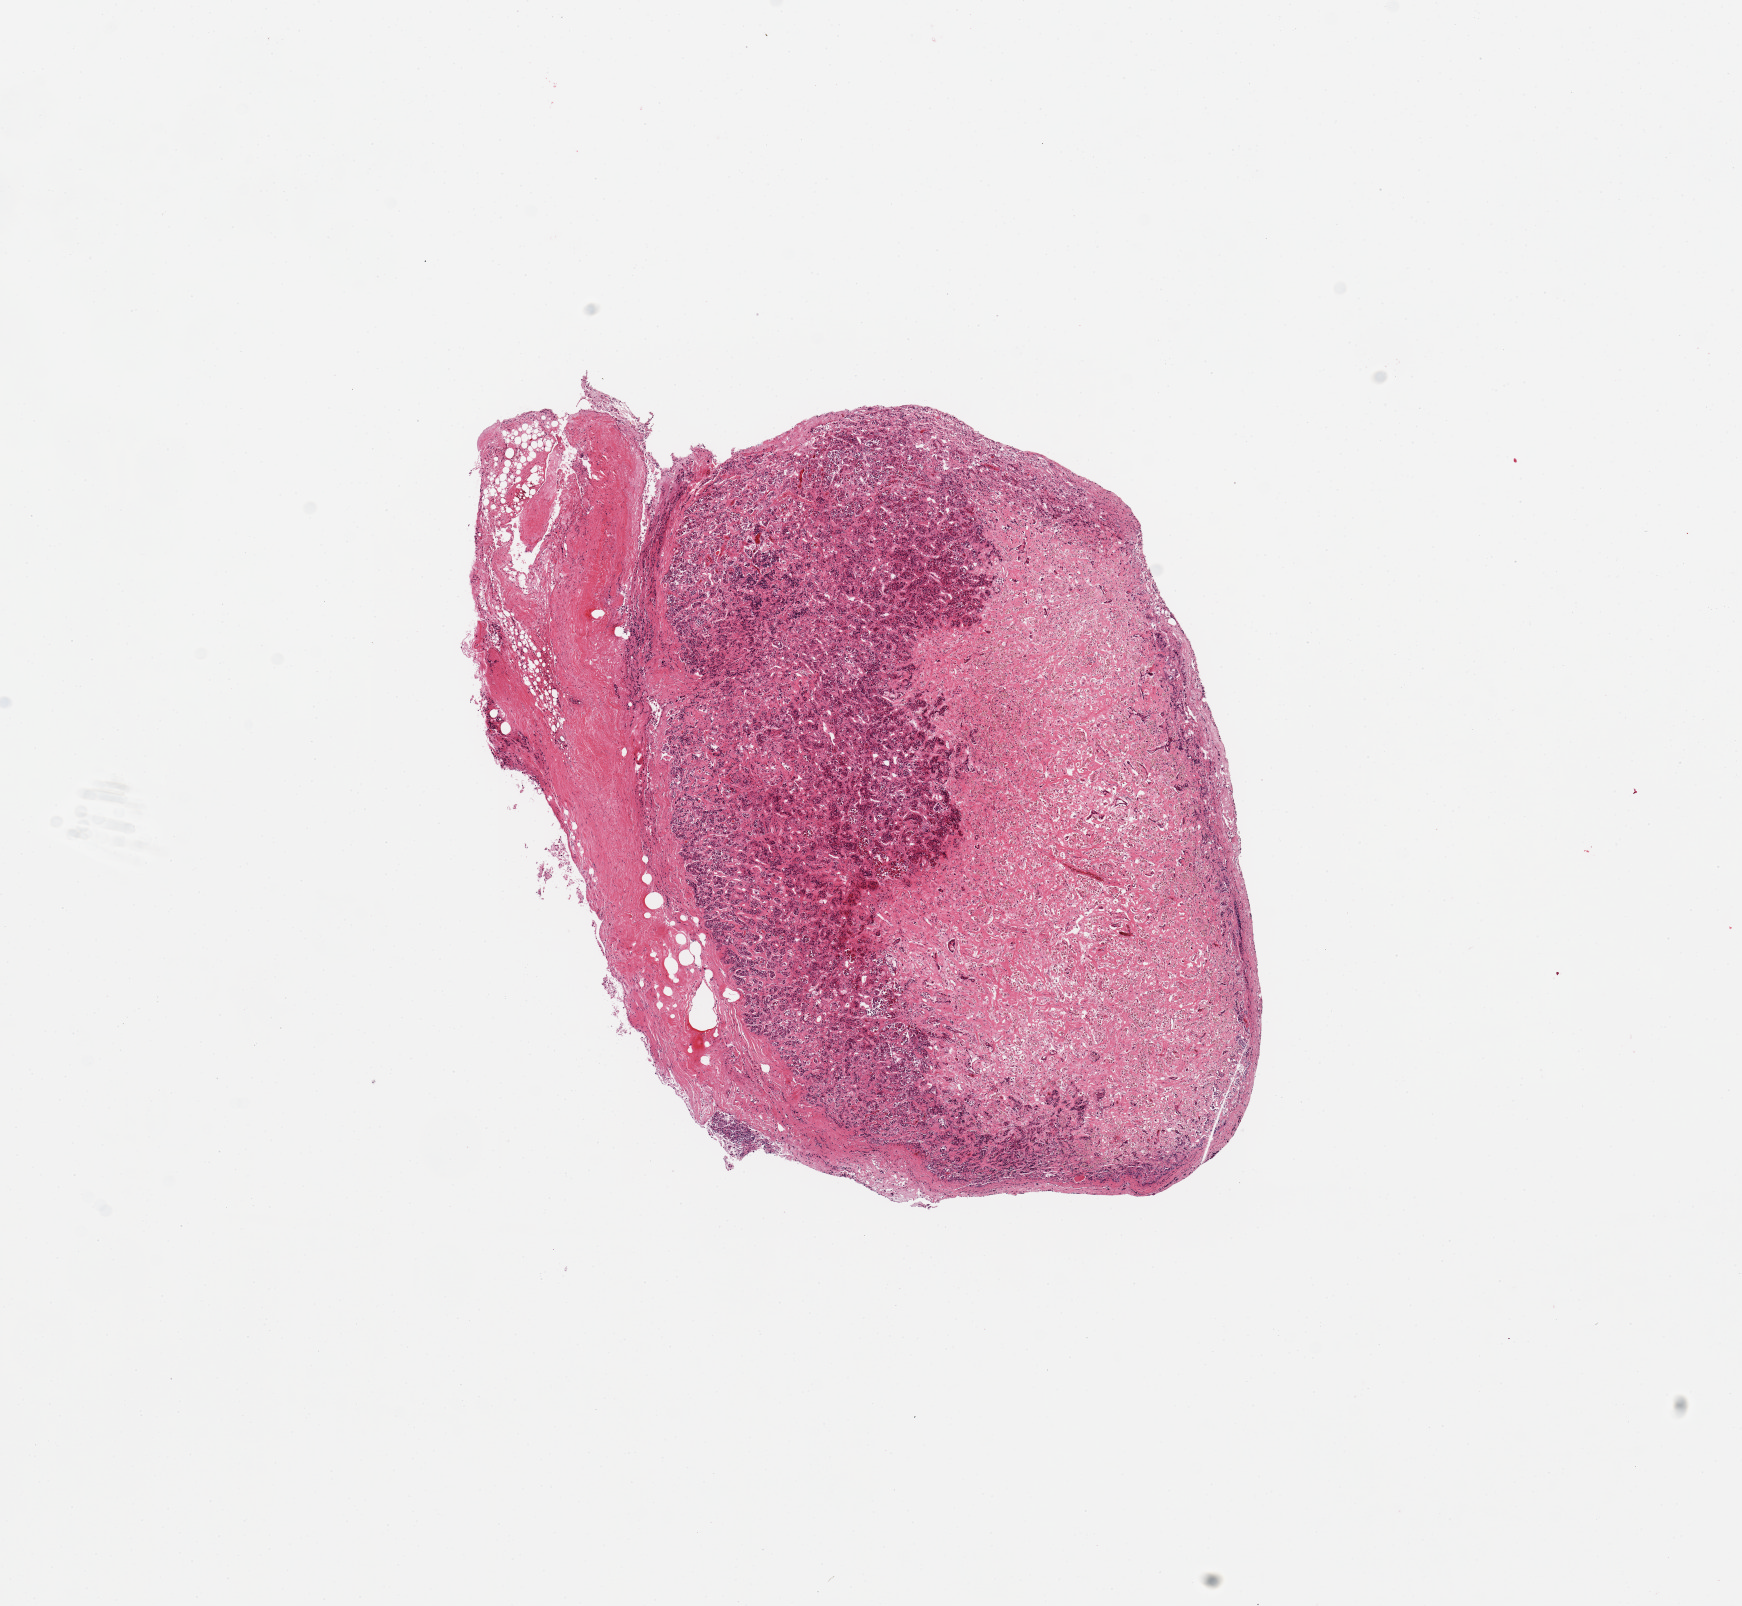
Whole-slide image, hematoxylin and eosin (H&E) stain — a low-resolution overview of the entire scanned area, about 13.8 x 12.7 mm (slide scanned at 20x). PAXgene-fixed, paraffin-embedded tissue. Sampled site (target tissue): pituitary. Tissue donor sample. Donor sex: male.
Pathologist's review note for this sample: 1 piece; adenohypophysis, ~40% is infarcted.